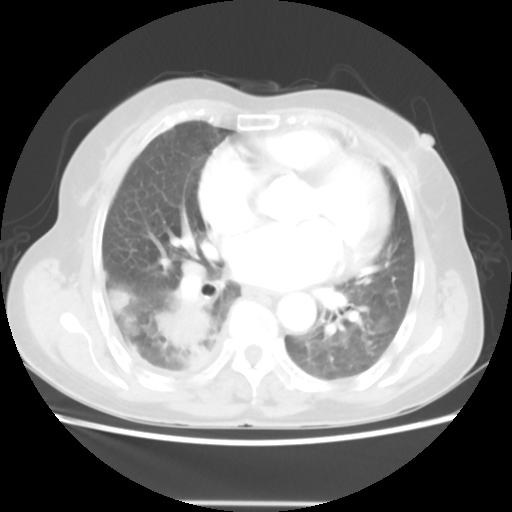
Chest CT, one axial slice. Slice 24 of 52 in the series (ordered by position). 140 kVp. Lung window (W 1500 / L -600 HU). 512 × 512 image matrix. Female patient, age 67 years. From the clinical record (not read from this slice): clinical TNM (as recorded): T3 N1 M1.
Outlined on this slice (bounding box drawn by a radiologist):
- lung tumour (recorded histology: adenocarcinoma): bounding box [x1, y1, x2, y2] px = [159, 298, 214, 372]